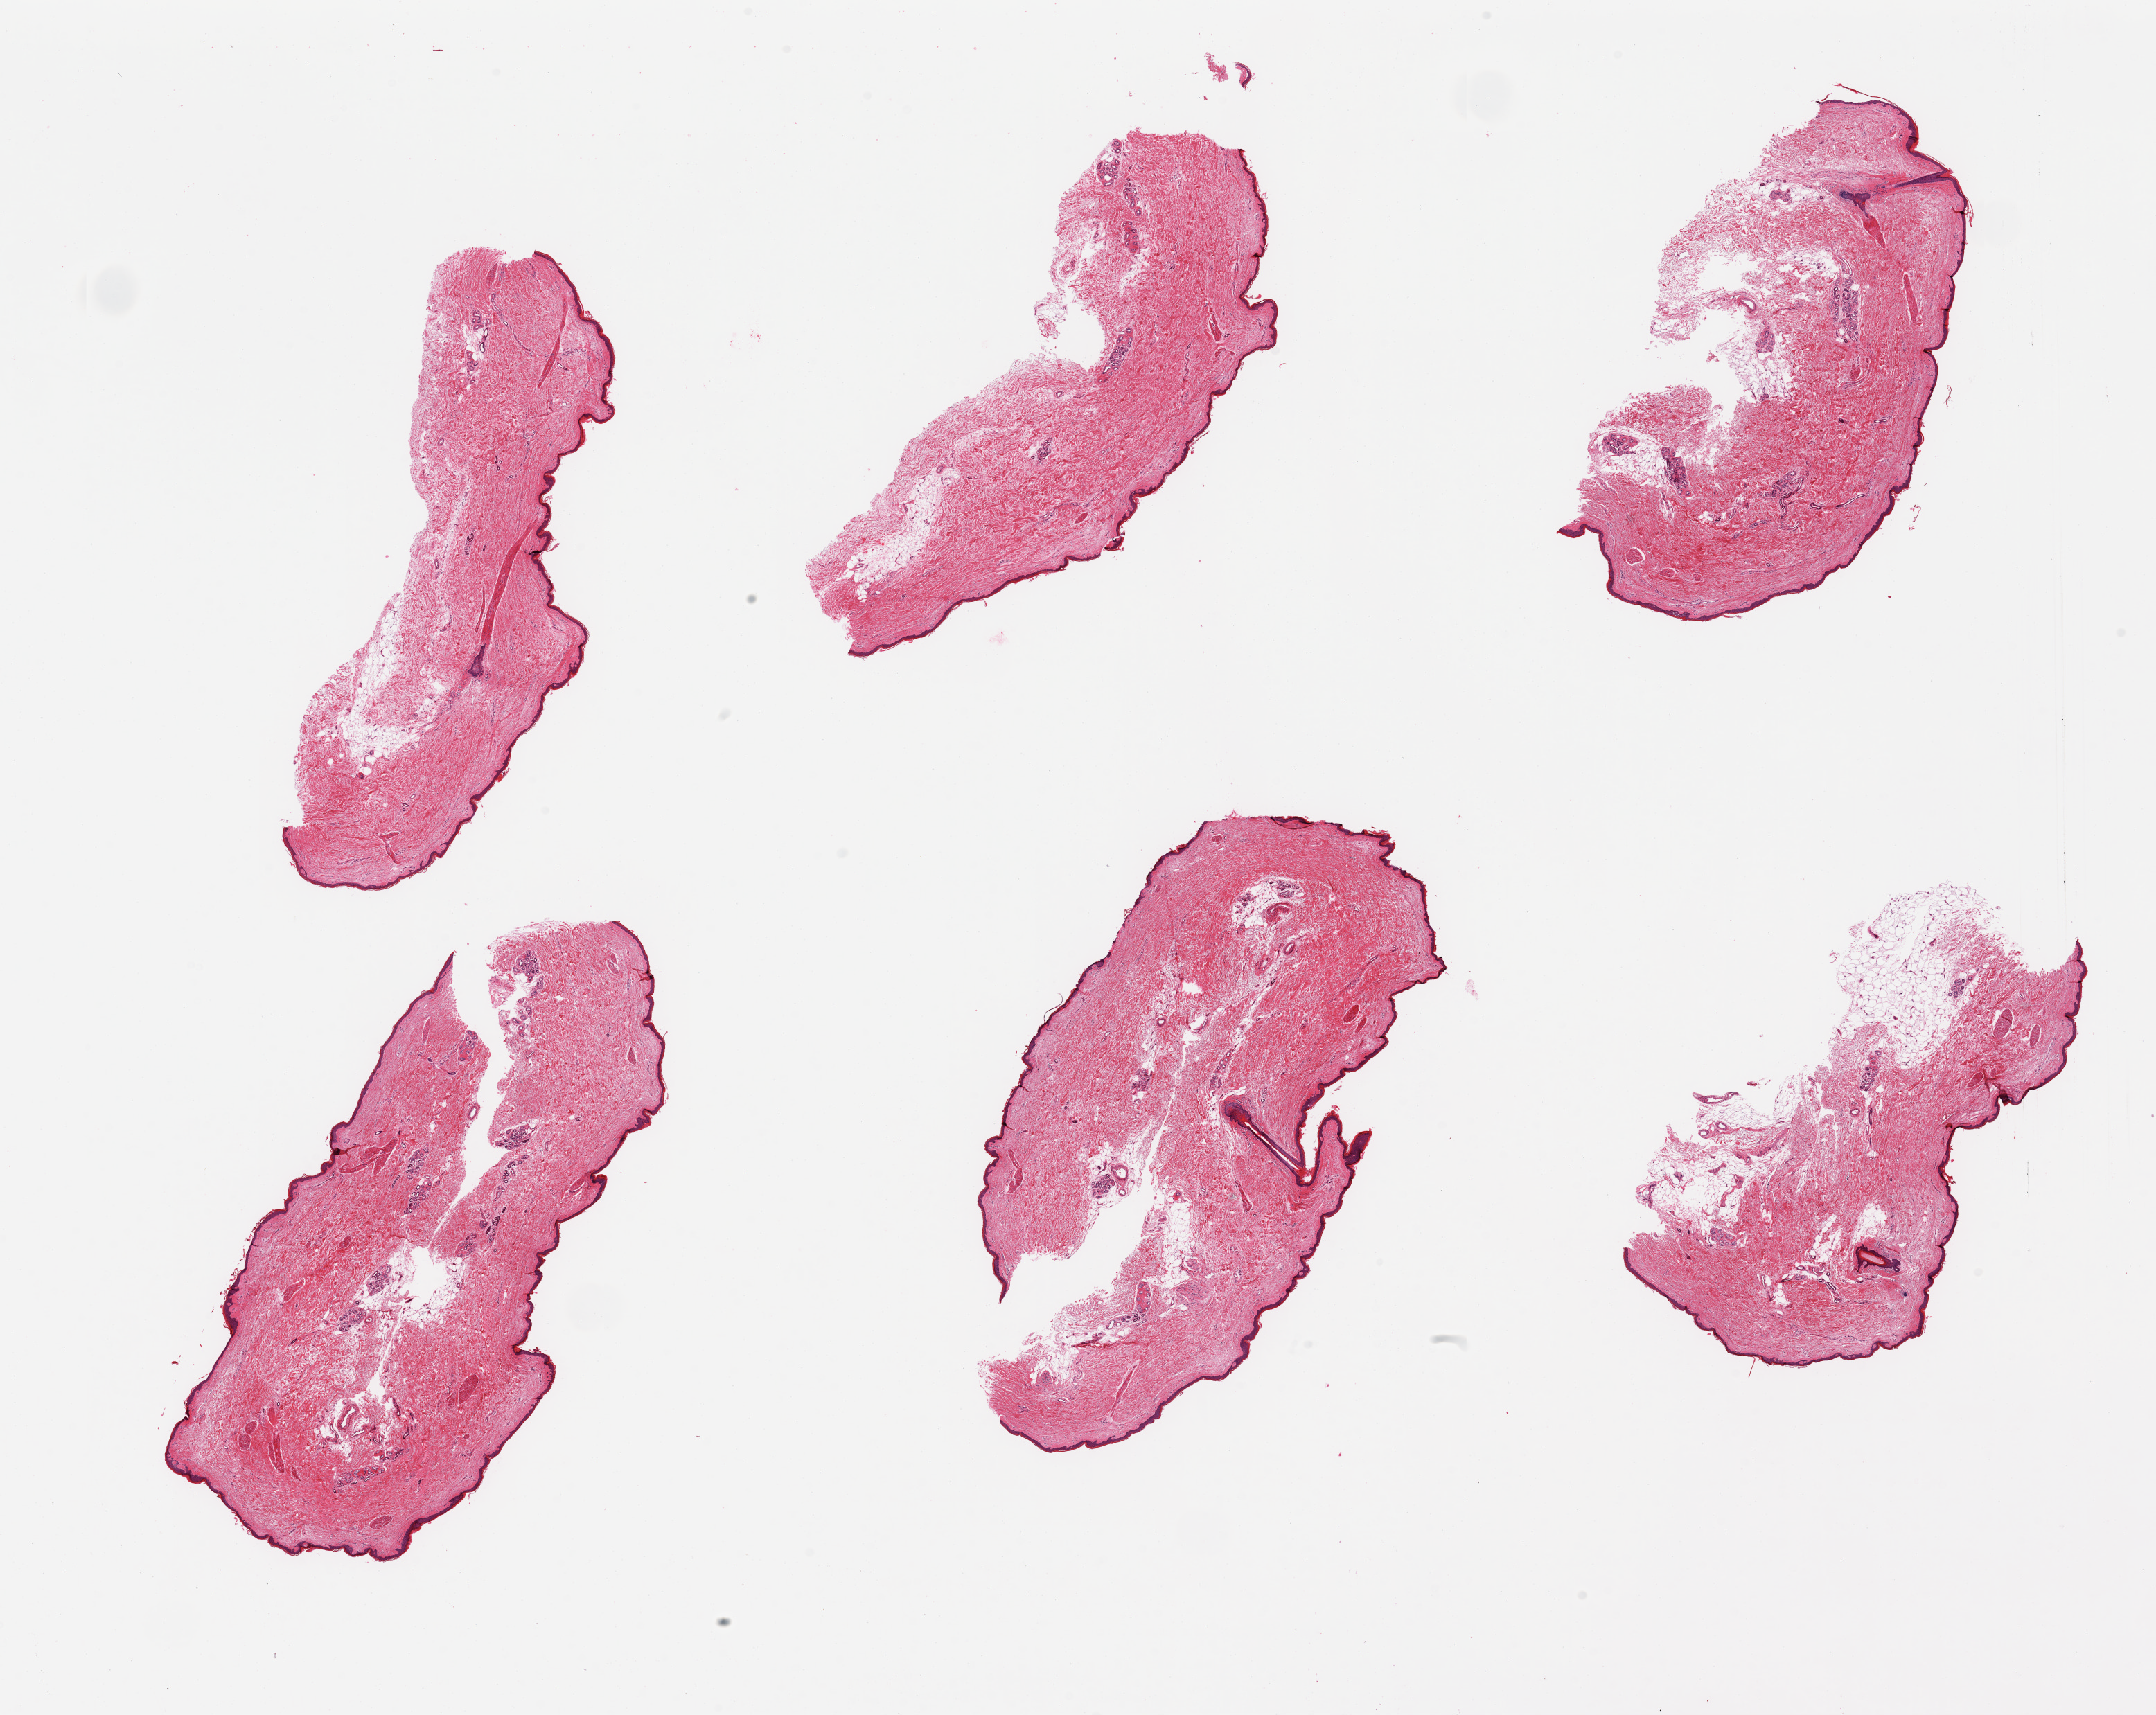
Whole-slide image, haematoxylin and eosin stain, low-resolution overview of the scanned area, about 24.6 x 19.6 mm; PAXgene-fixed paraffin-embedded (PFPE) section; target tissue: skin of lower leg; donor tissue sample. Donor: male.
Reviewer comment on this tissue sample: 6 pieces; 10% dermal fat; some thickening of collagen bundles and atrophy of adnexal structures, but no clear-cut signs of dermal scleroderma.